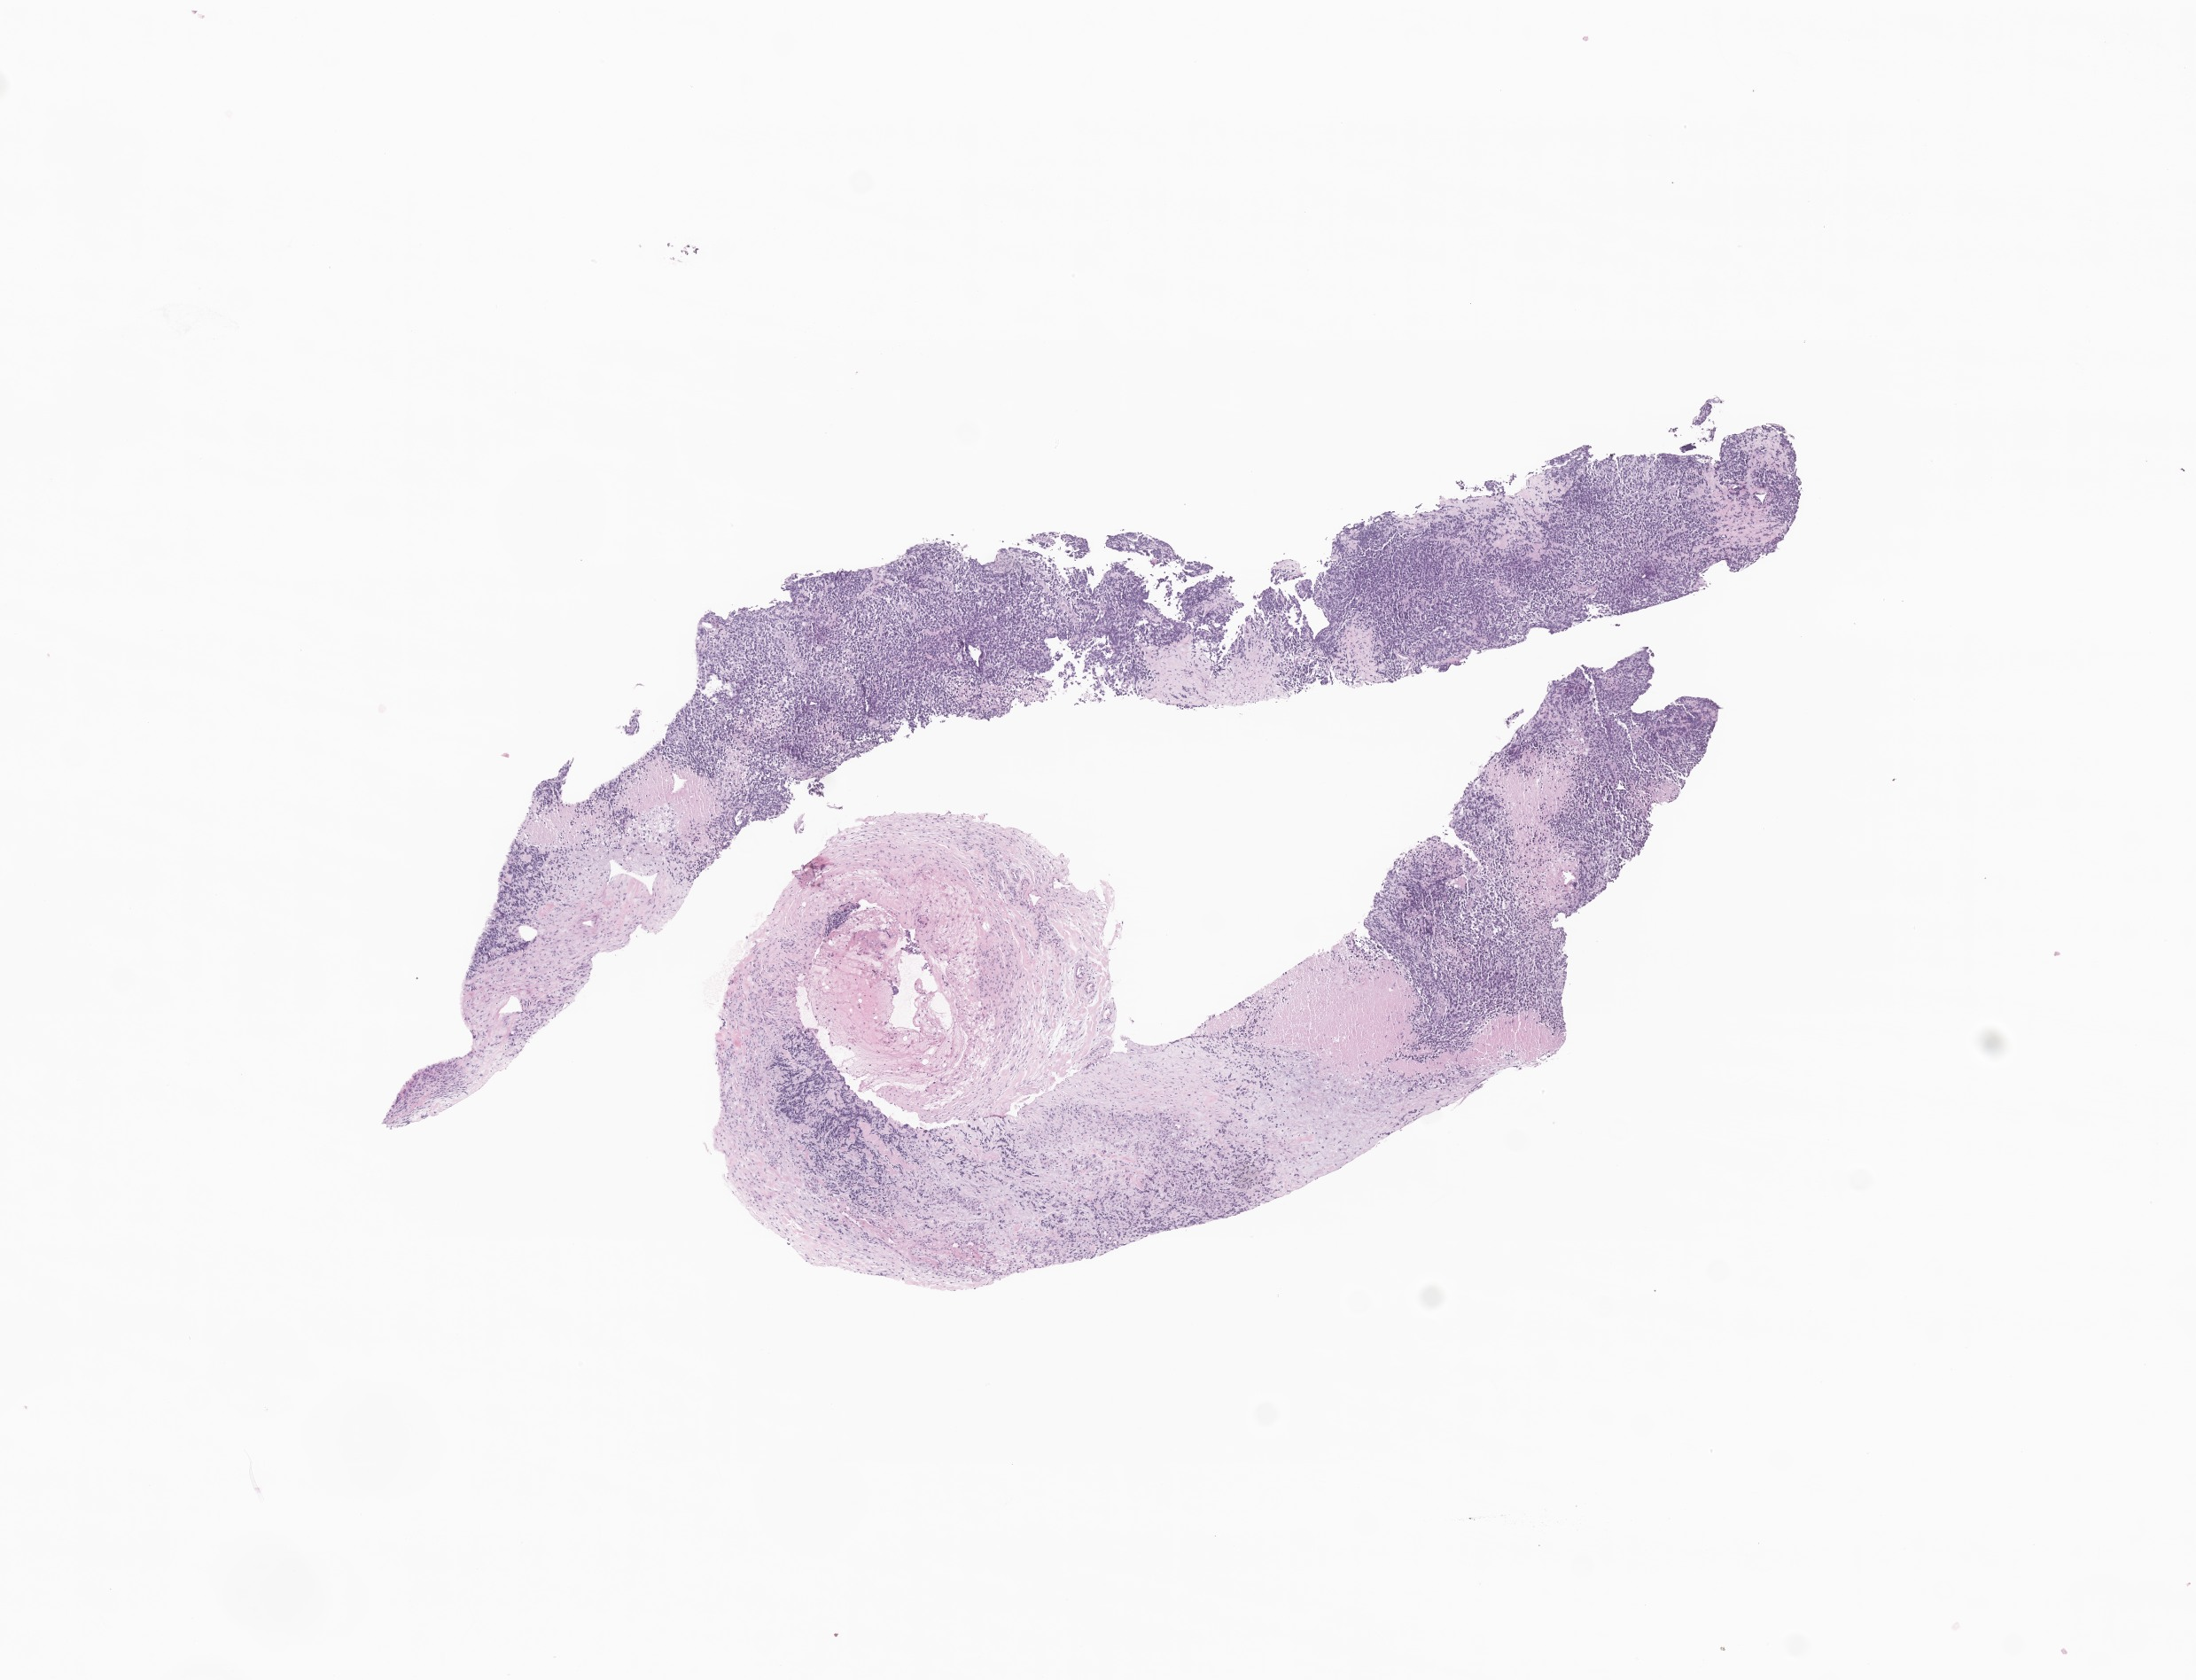
H&E whole-slide image of tumor tissue from the prostate — whole scanned area (about 10.4 x 8.0 mm) shown as a low-resolution overview. Formalin-fixed paraffin-embedded section. Patient male; age 121 months (10 years 1 month).
Diagnosis: Rhabdomyosarcoma, NOS.